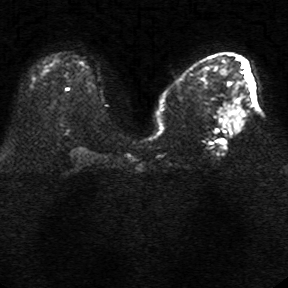
Breast MRI, one axial slice; slice 13 of 34 in the series (ordered by position); diffusion-weighted series; image 2 of 4 stored at this slice position (different b-values; order by instance number); 1.5 T; 5 mm slice thickness; 288 × 288 image matrix, field of view 340 × 340 mm. Female patient.
Annotated regions visible in this slice (outlined manually by an expert reader):
- tumour on diffusion-weighted imaging: box from (x=226, y=104) to (x=241, y=123) px